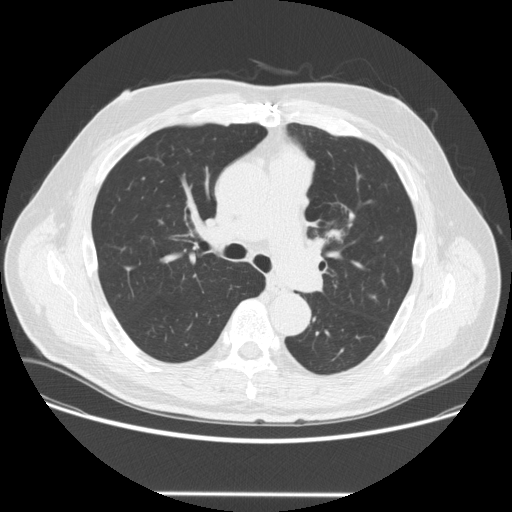
Low-dose screening chest CT, axial slice, third annual screen, lung window (W 1500 / L -600 HU), 2.5 mm slice thickness, standard (soft-tissue) reconstruction kernel (STANDARD), 120 kVp, slice 88 of 253 in the series. Male participant, aged 66 years at enrolment. Former smoker at enrolment.
Expert reader's lesion annotation, bounding box <310,203,363,253> (left, top, right, bottom; pixels). The screening reader recorded 2 non-calcified nodules or masses ≥4 mm on this exam; which of them this box marks is not recorded.